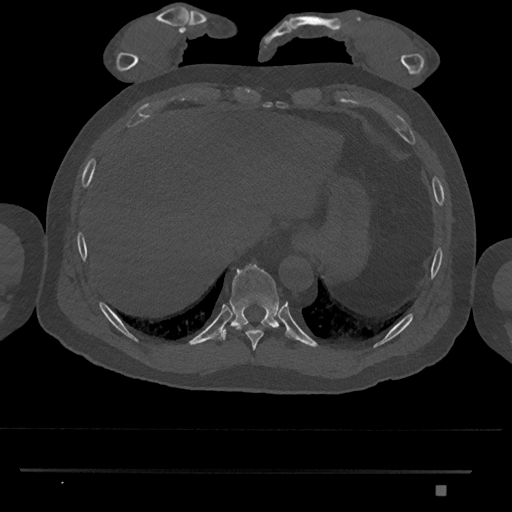
CT including the spine, one axial slice. Position 1025 of 1134 along the scan axis. 120 kVp. Bone window (W 1800 / L 400 HU). 0.5 mm slice thickness. 512 × 512 image matrix, field of view 429 × 429 mm. Male patient, age 65 years. From the clinical record (not read from this slice): primary cancer: prostate.
Annotated regions visible in this slice (semi-automatic segmentation, software-assisted and operator-edited):
- T10 vertebra: bounding box [x1, y1, x2, y2] px = [220, 264, 279, 340]
- T9 vertebra: [234, 325, 273, 351]